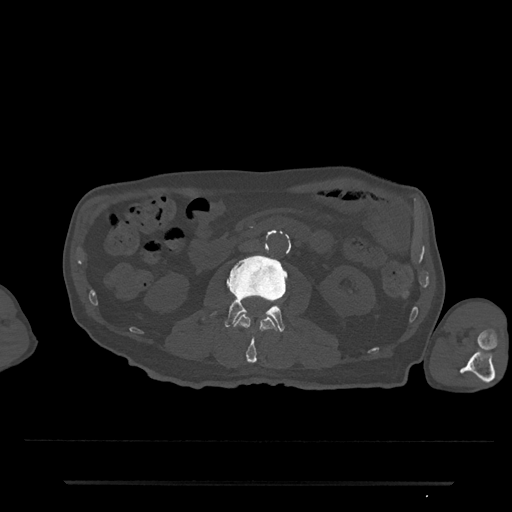
CT including the spine, one axial slice. 120 kVp. Bone window (W 1800 / L 400 HU). 0.5 mm slice thickness. 512 × 512 image matrix, field of view 427 × 427 mm. Patient: male, 74 years. From the clinical record (not read from this slice): primary cancer: prostate.
Structures marked on this image (semi-automatic segmentation, software-assisted and operator-edited):
- L2 vertebra: box from (x=234, y=314) to (x=277, y=364) px
- L3 vertebra: (x=202, y=255)–(x=287, y=332)